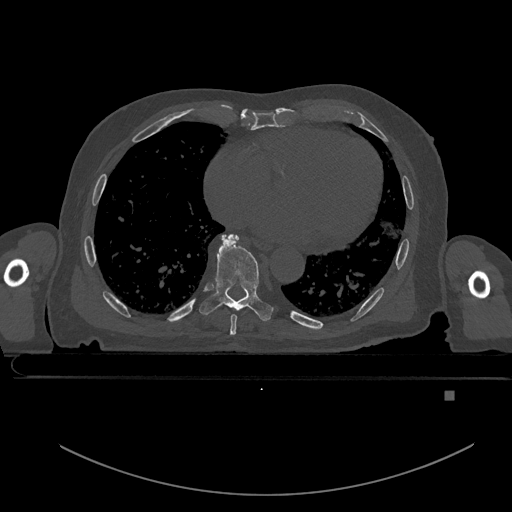
CT including the spine, one axial slice; position 211 of 969 along the scan axis; bone window (W 1800 / L 400 HU); 512 × 512 image matrix, field of view 456 × 456 mm. Patient: male, 82 years. From the clinical record (not read from this slice): primary cancer: prostate; vertebrae with lytic lesions (as recorded): T11, T9, T8, T2.
Structures marked on this image (semi-automatically segmented with operator editing):
- T7 vertebra: bounding box (x1, y1, x2, y2) in pixels: (229, 236, 237, 335)
- T8 vertebra: (199, 234, 273, 321)